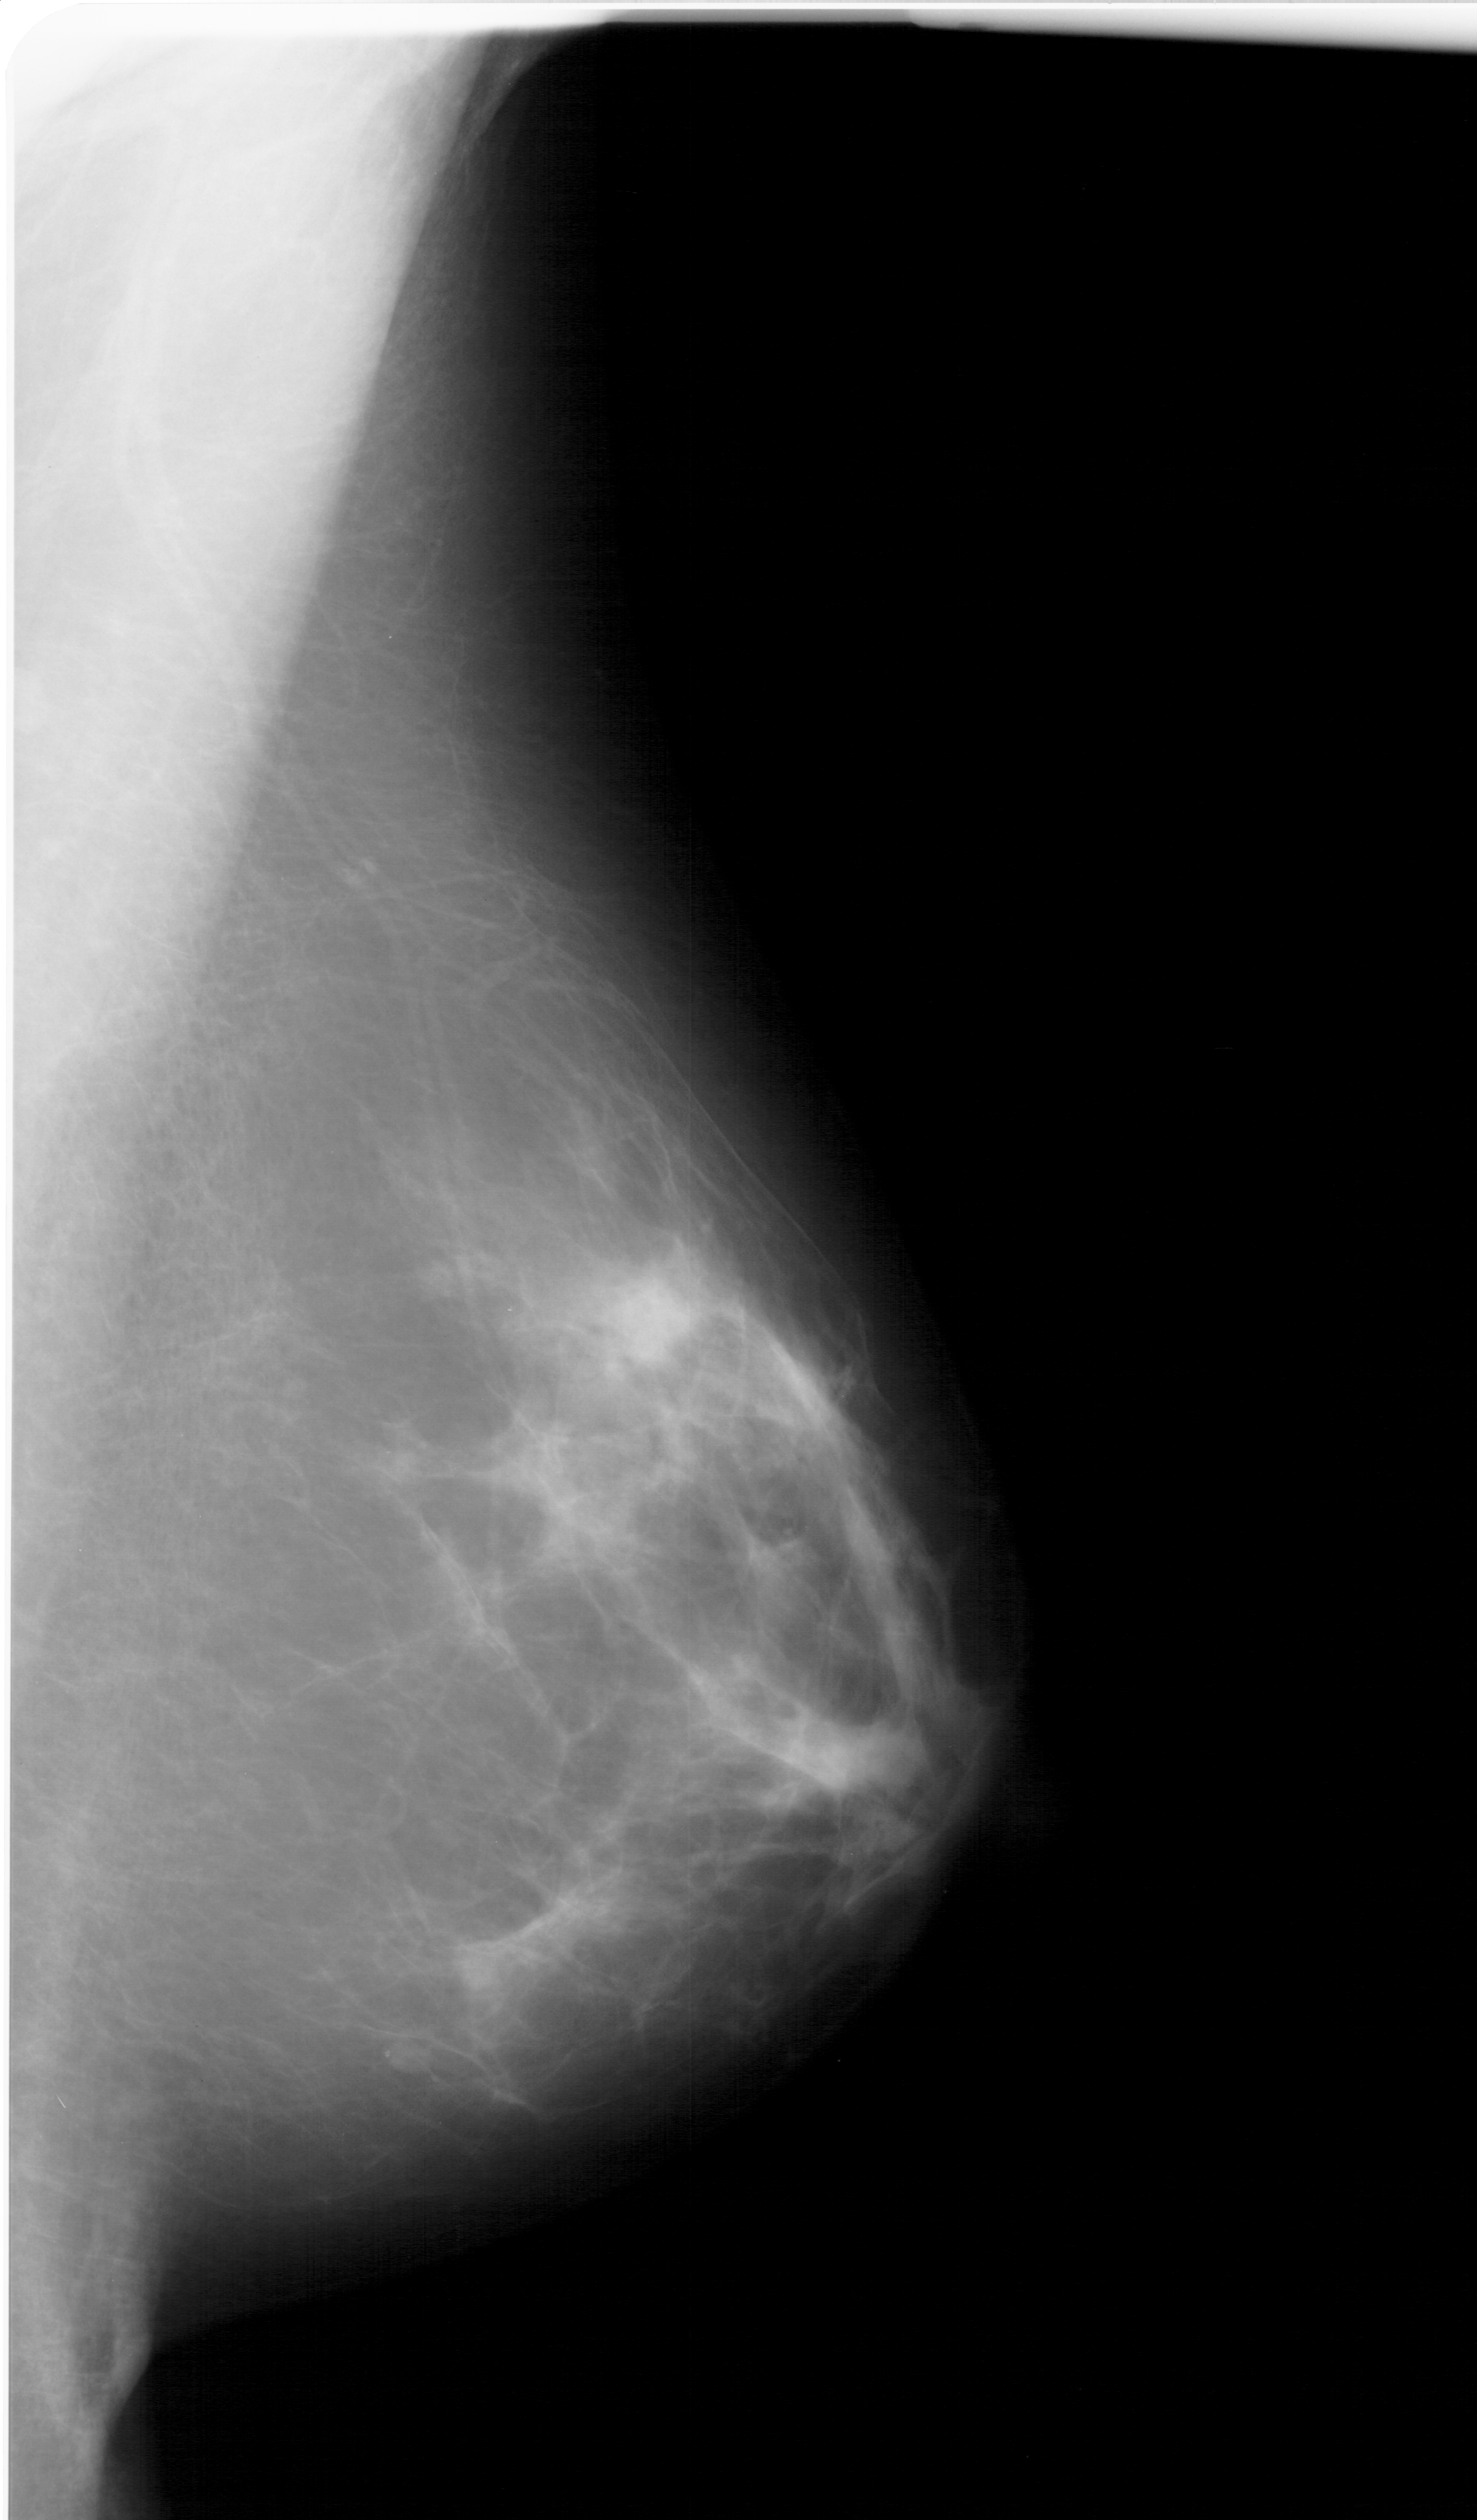
Scanned film-screen mammogram; right breast; MLO view; breast composition: heterogeneously dense (BI-RADS density category 3 of 4); 1477 × 2520 image matrix.
Expert-marked regions of interest on this film, with their recorded descriptors:
- mass, shape irregular, margins ill defined; BI-RADS assessment category 4; subtlety rating 2 on a 1 (subtle) to 5 (obvious) scale; pathology (as recorded): benign: bounding box <515,1243,714,1404> (left, top, right, bottom; pixels)